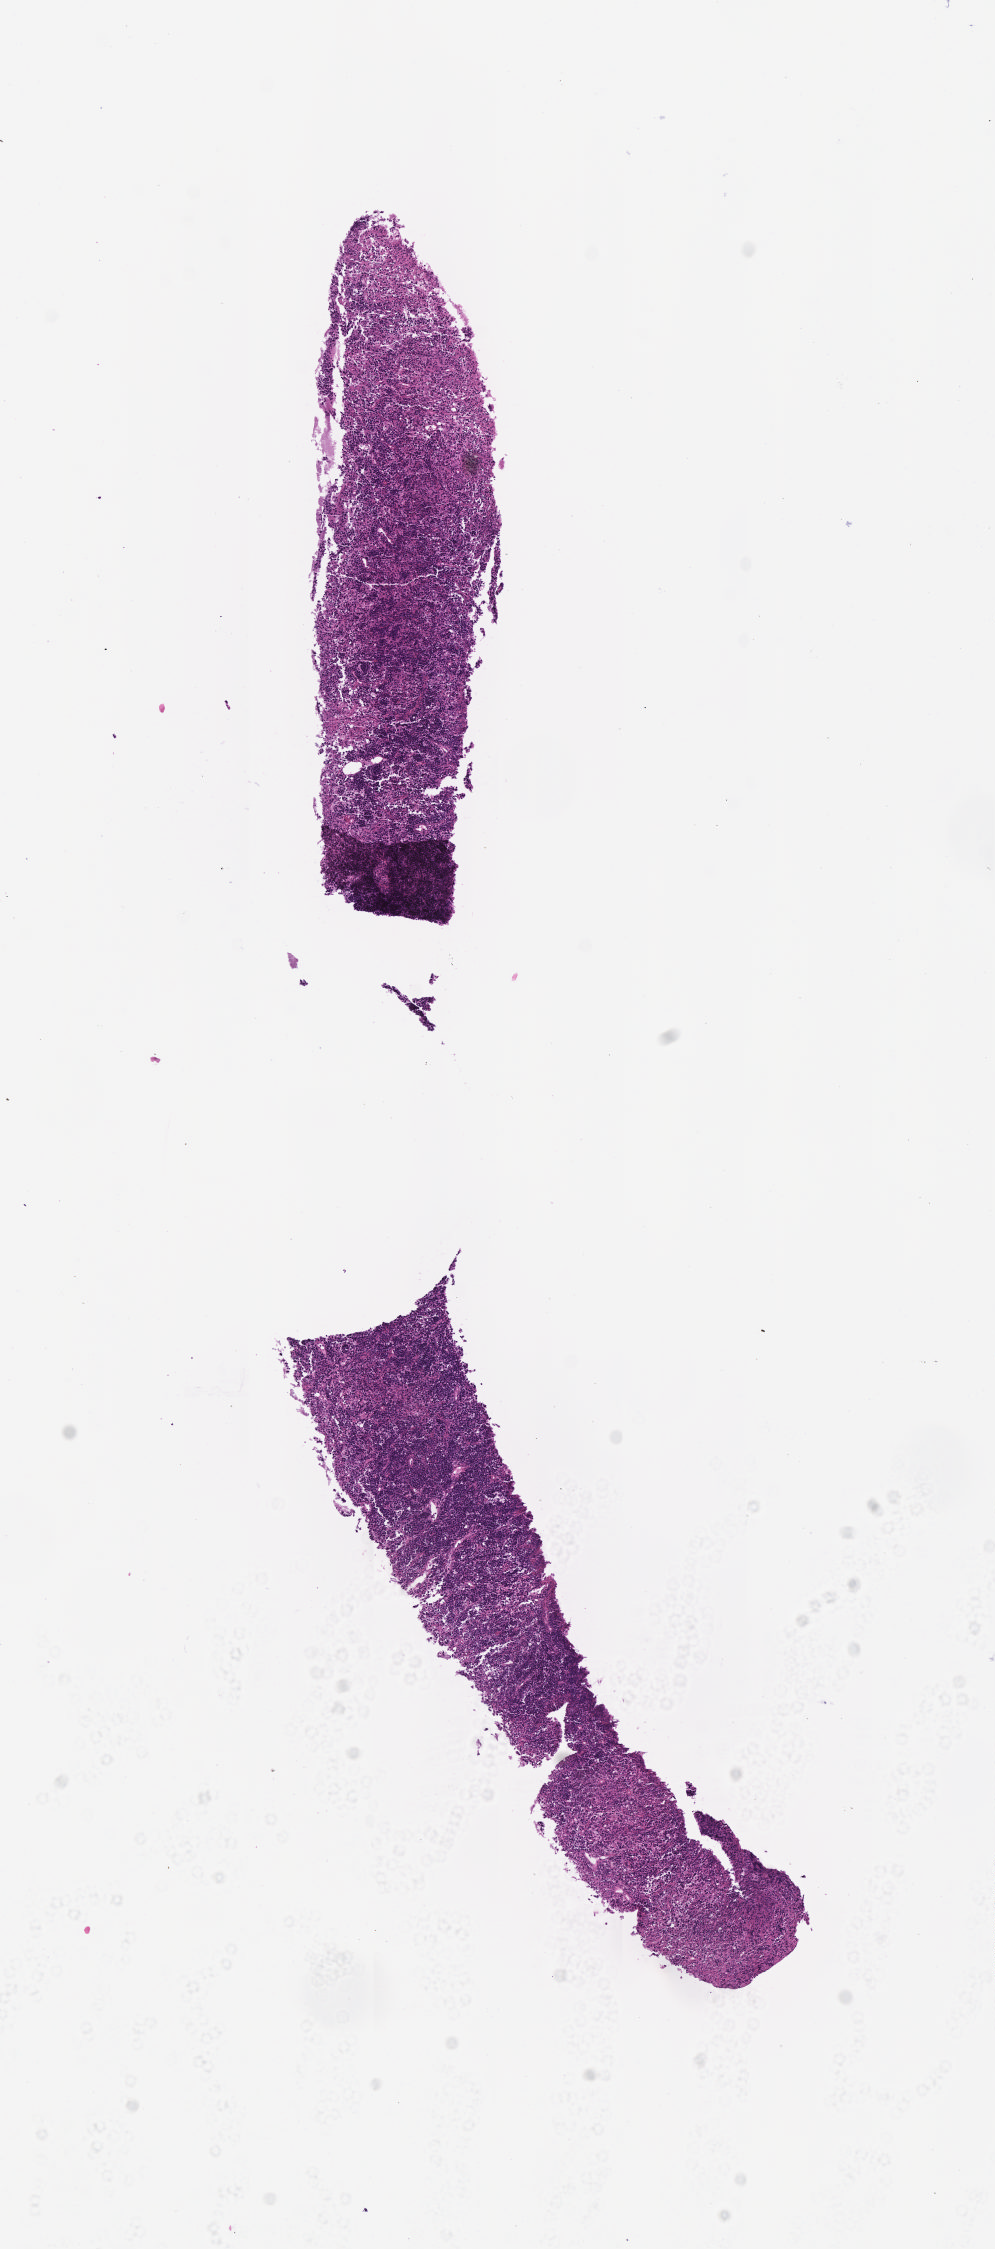
Haematoxylin and eosin whole-slide image, whole scanned area (about 4.0 x 9.1 mm) shown as a low-resolution overview. Male patient.
Specimen: tumor tissue.